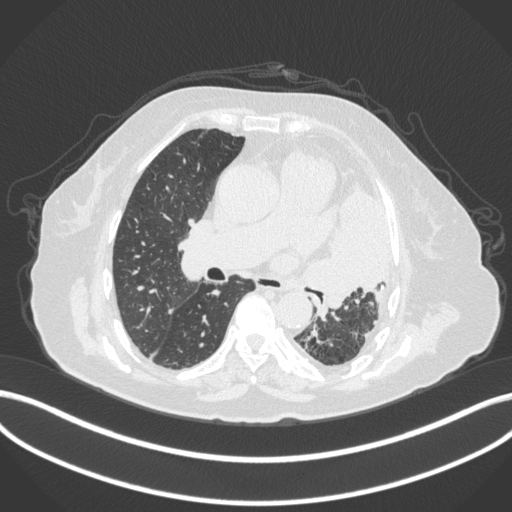
Chest CT, one axial slice; position 205 of 399 along the scan axis; reconstruction kernel B31f; lung window (W 1500 / L -600 HU); 512 × 512 image matrix, field of view 400 × 400 mm. Patient: female, 75 years. From the clinical record (not read from this slice): clinical TNM (as recorded): T3 N3 M1.
Annotated regions visible in this slice (rectangle marked by the reading radiologist):
- lung tumour (recorded histology: adenocarcinoma): box from (x=298, y=187) to (x=401, y=311) px